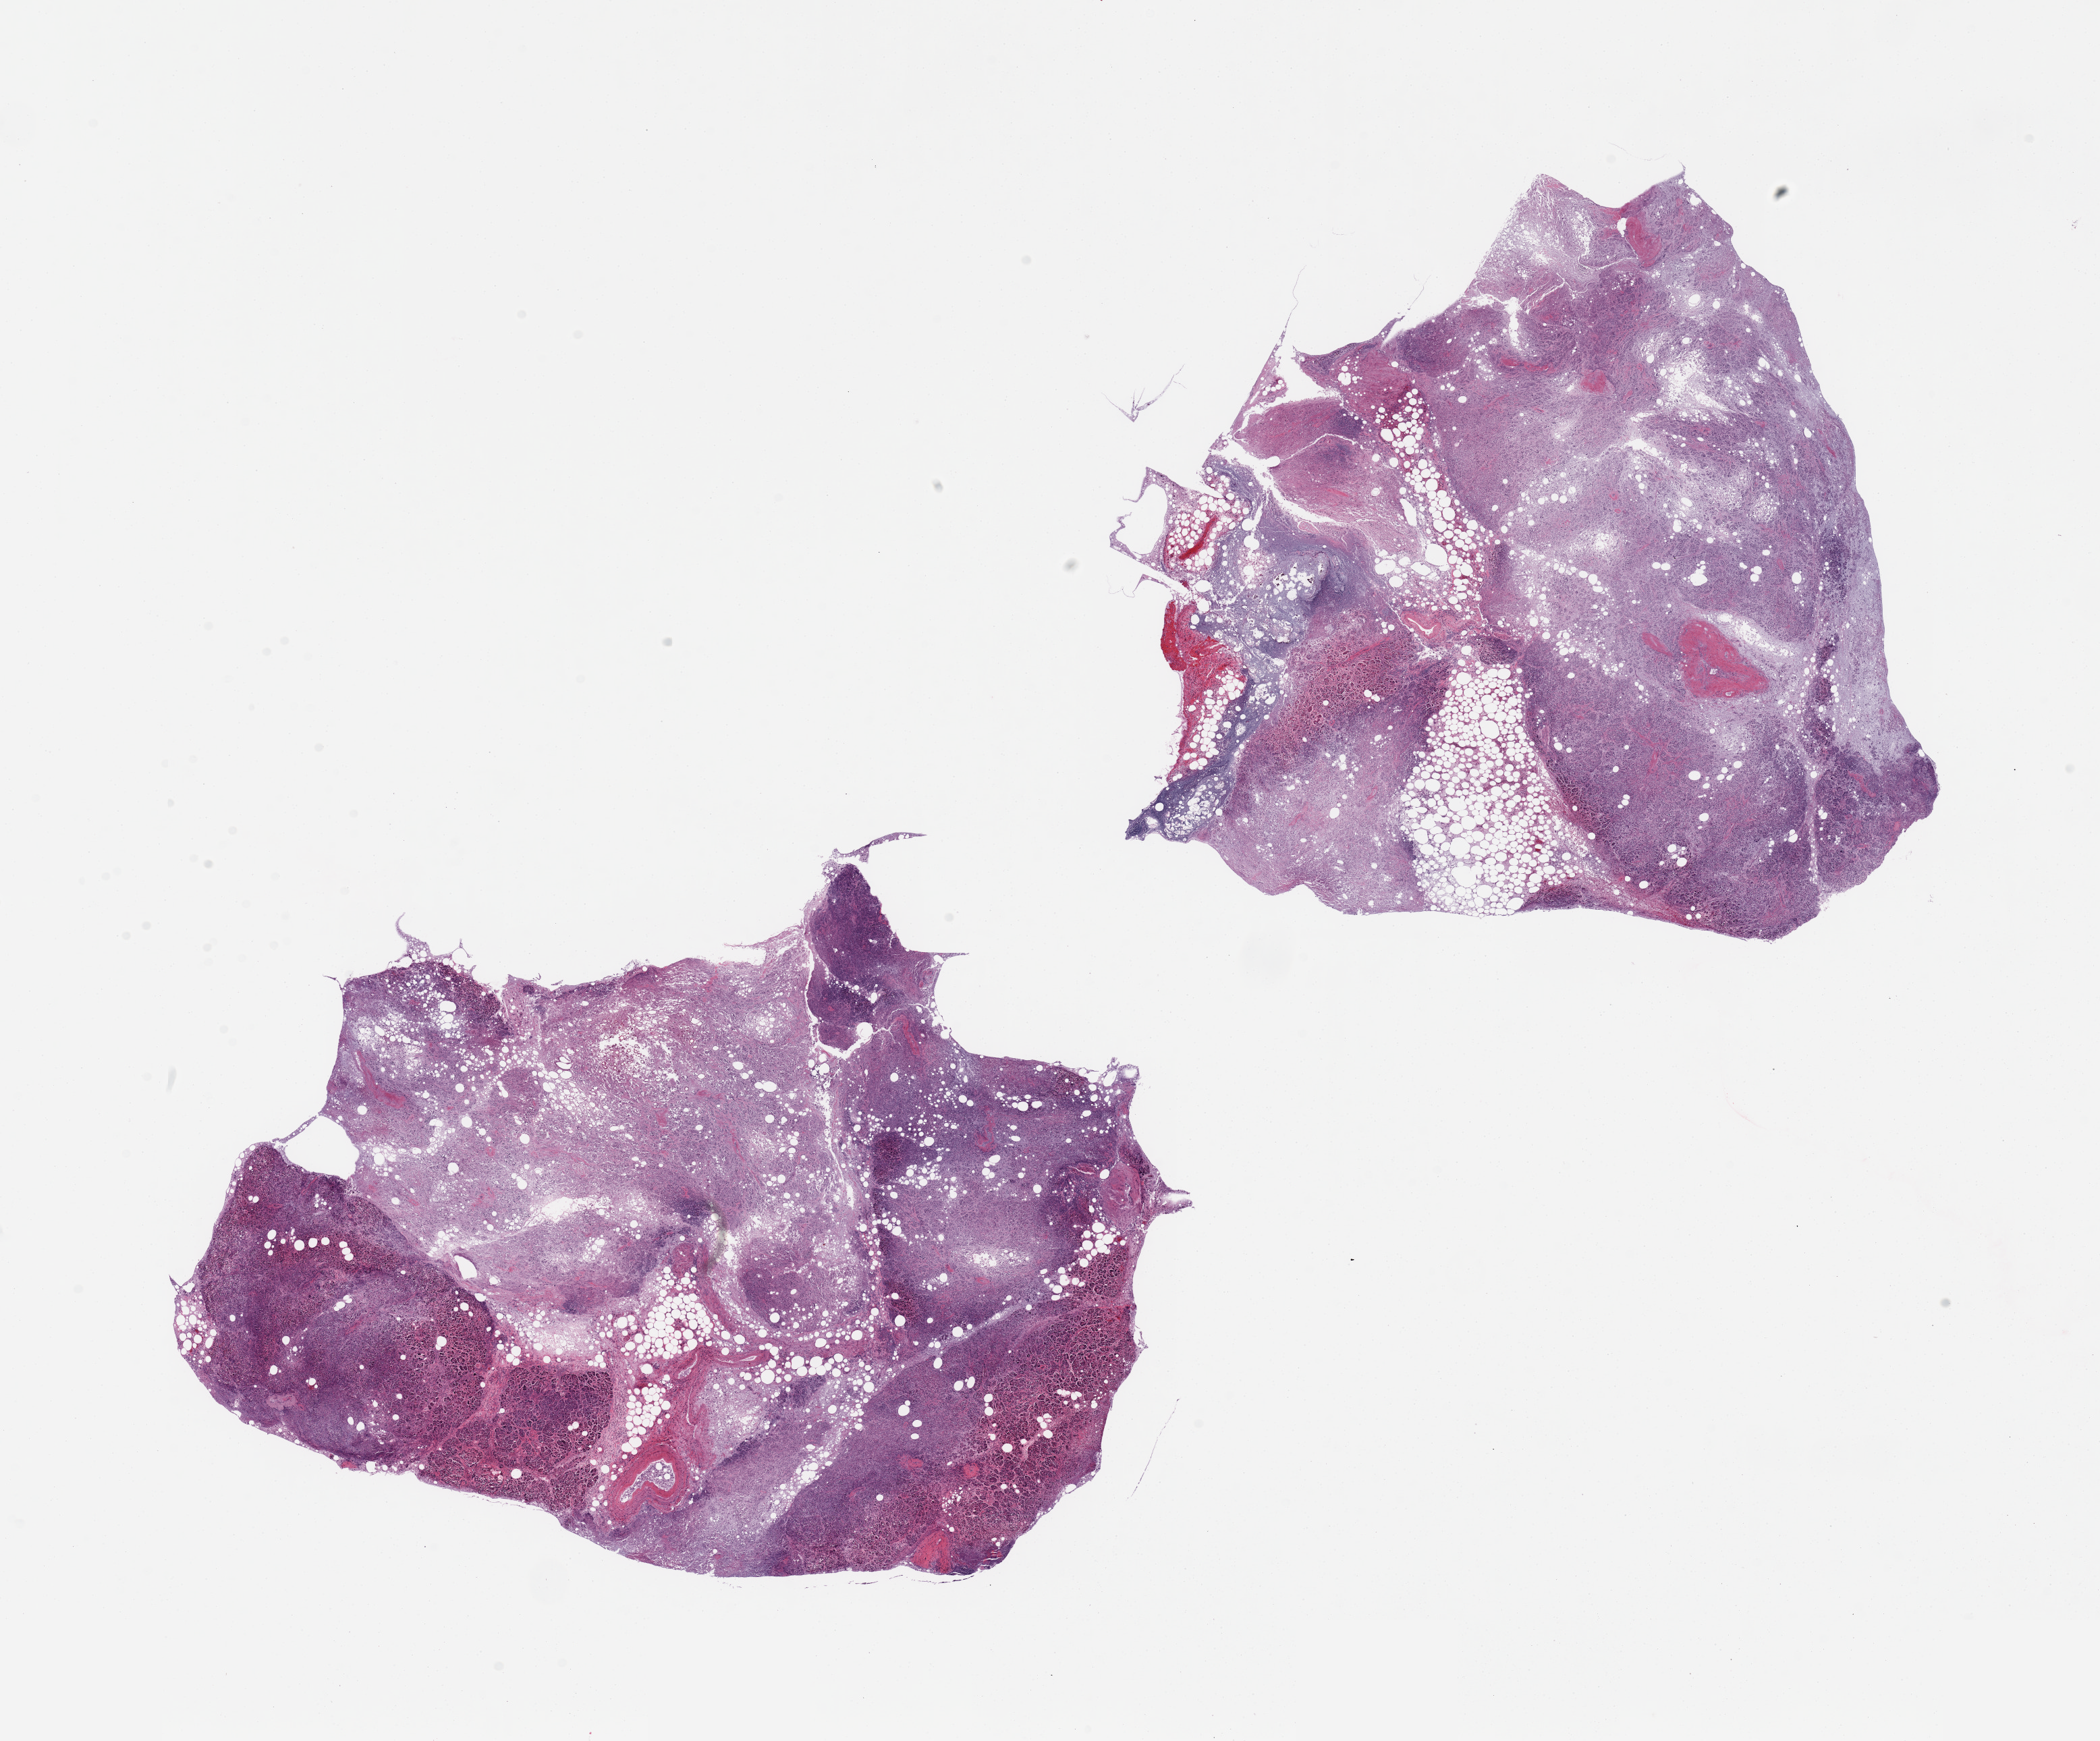
Whole-slide image, hematoxylin and eosin (H&E) stain, low-resolution overview of the scanned area, about 24.6 x 20.4 mm.
Specimen: PAXgene-fixed paraffin-embedded (PFPE) section; sampled site (target tissue): pancreas; tissue donor sample.